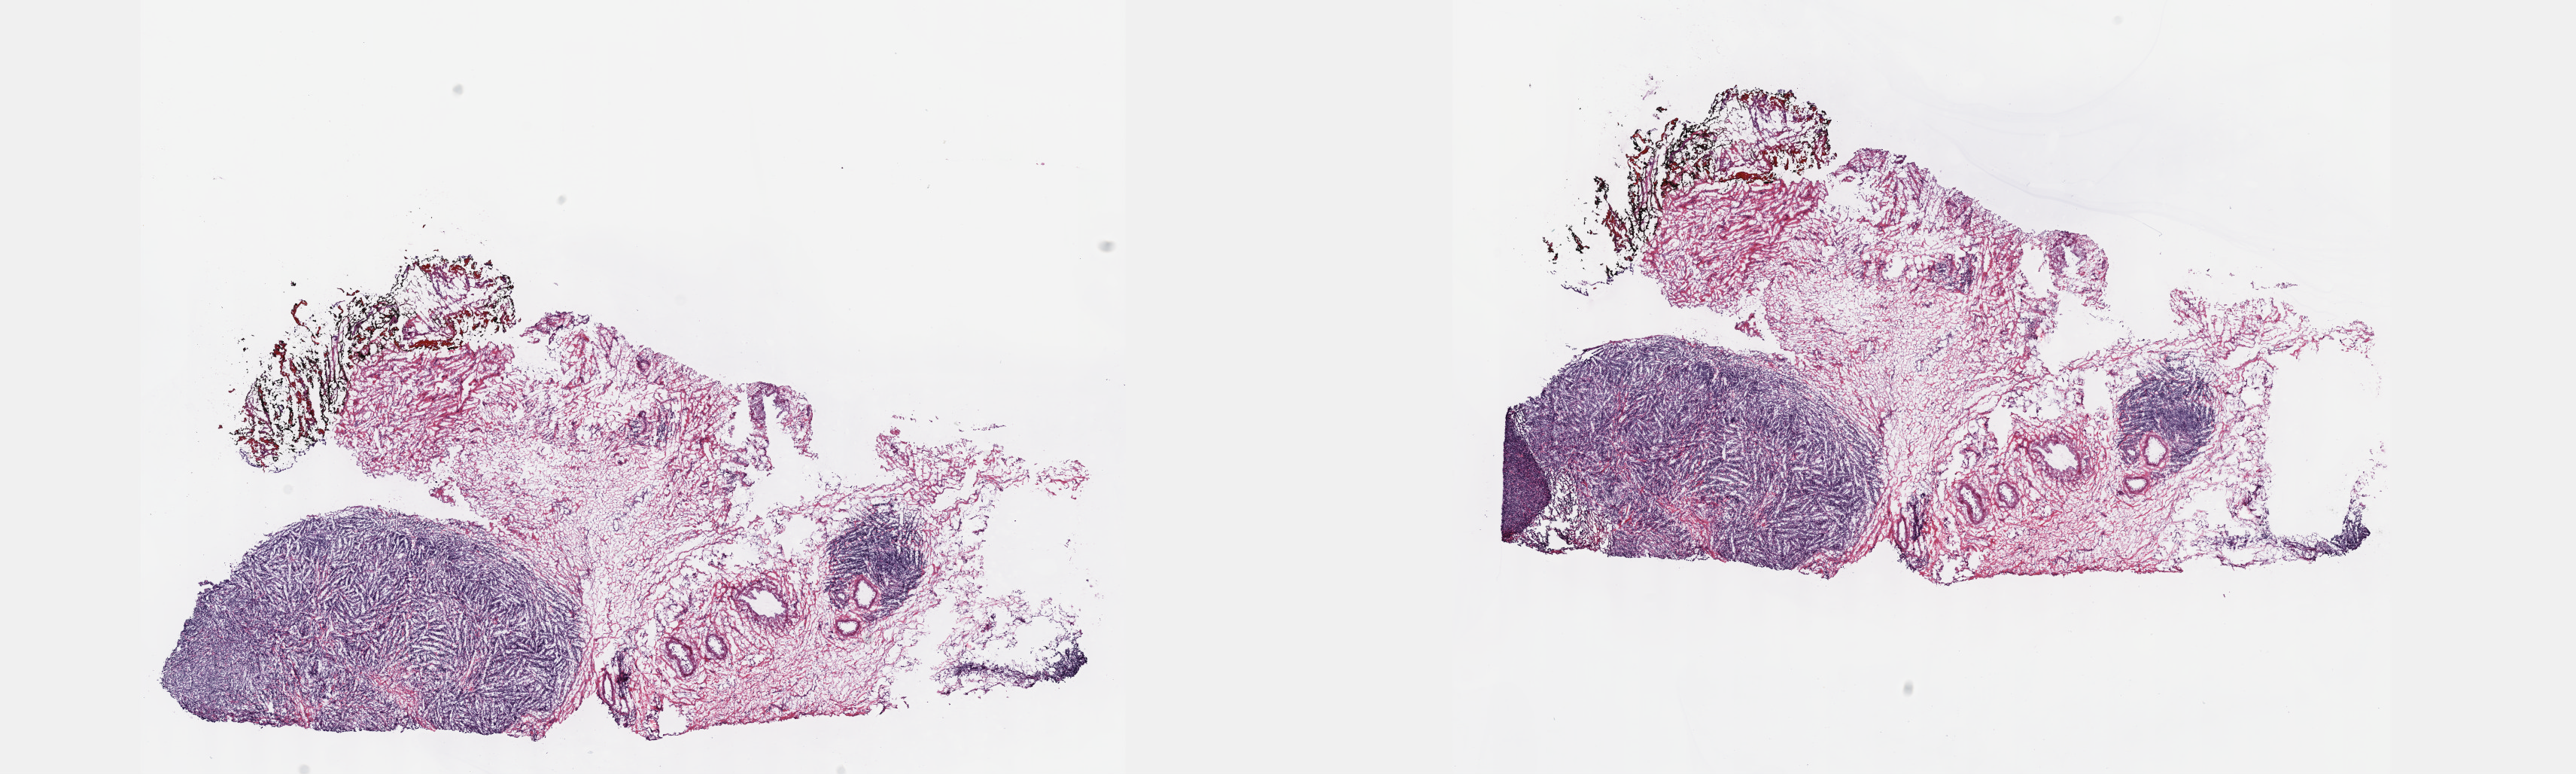
Digitized Hematoxylin and eosin (H&E) stained tissue section (whole slide), whole scanned area (about 27.7 x 8.3 mm, slide scanned at 40x) shown as a low-resolution overview; frozen section; primary tumour sample from the thymus. Female patient; age at initial diagnosis 67 years. Composition of this section per pathologist review: tumour cells 50%, tumour nuclei 60%, normal cells 50%, stromal cells 0%, necrosis 0%. Inflammatory infiltration, as recorded: lymphocyte infiltration 0%, monocyte infiltration 0%, neutrophil infiltration 0%.
- histologic diagnosis: Thymic carcinoma, NOS